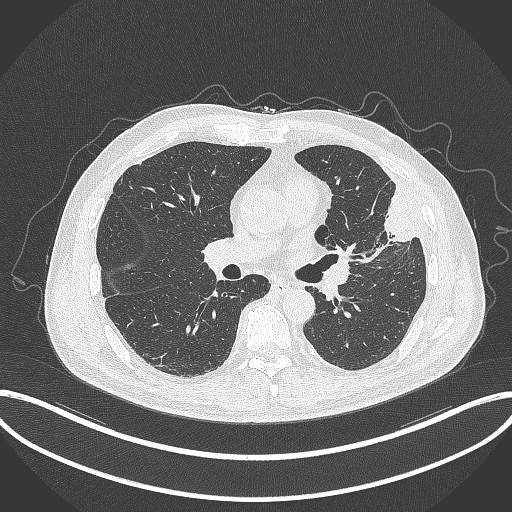
Chest CT, one axial slice. Slice 181 of 382 in the series (ordered by position). 120 kVp. Lung window (W 1500 / L -600 HU). 1 mm slice thickness. 512 × 512 image matrix. Patient: male, 64 years. From the clinical record (not read from this slice): clinical TNM (as recorded): T4 N1 M0; histopathological grade: G3.
Outlined on this slice (rectangle marked by the reading radiologist):
- lung tumour (recorded histology: adenocarcinoma): box from (x=370, y=188) to (x=422, y=250) px